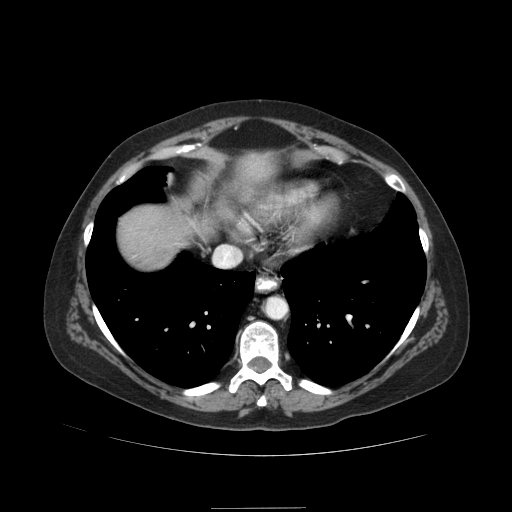
Contrast-enhanced abdominal CT (liver protocol), one axial slice; slice 79 of 89 in the series (ordered by position); reconstruction kernel STANDARD; 120 kVp; soft-tissue window (W 400 / L 40 HU); 2.5 mm slice thickness; 512 × 512 image matrix, field of view 400 × 400 mm. Case-level facts recorded for this patient, not image findings: diagnosis: hepatocellular carcinoma (patient treated with transarterial chemoembolisation; whether this scan precedes or follows treatment is not stated here); TNM stage (as recorded): Stage-IIIB; Child-Pugh class: A; tumour nodularity: multinodular.
Outlined on this slice (semi-automatically segmented with operator editing):
- liver parenchyma outside the tumour (the mass and vessels are separate outlines, so this box may not span the whole liver): bounding box (x1, y1, x2, y2) in pixels: (118, 152, 274, 267)